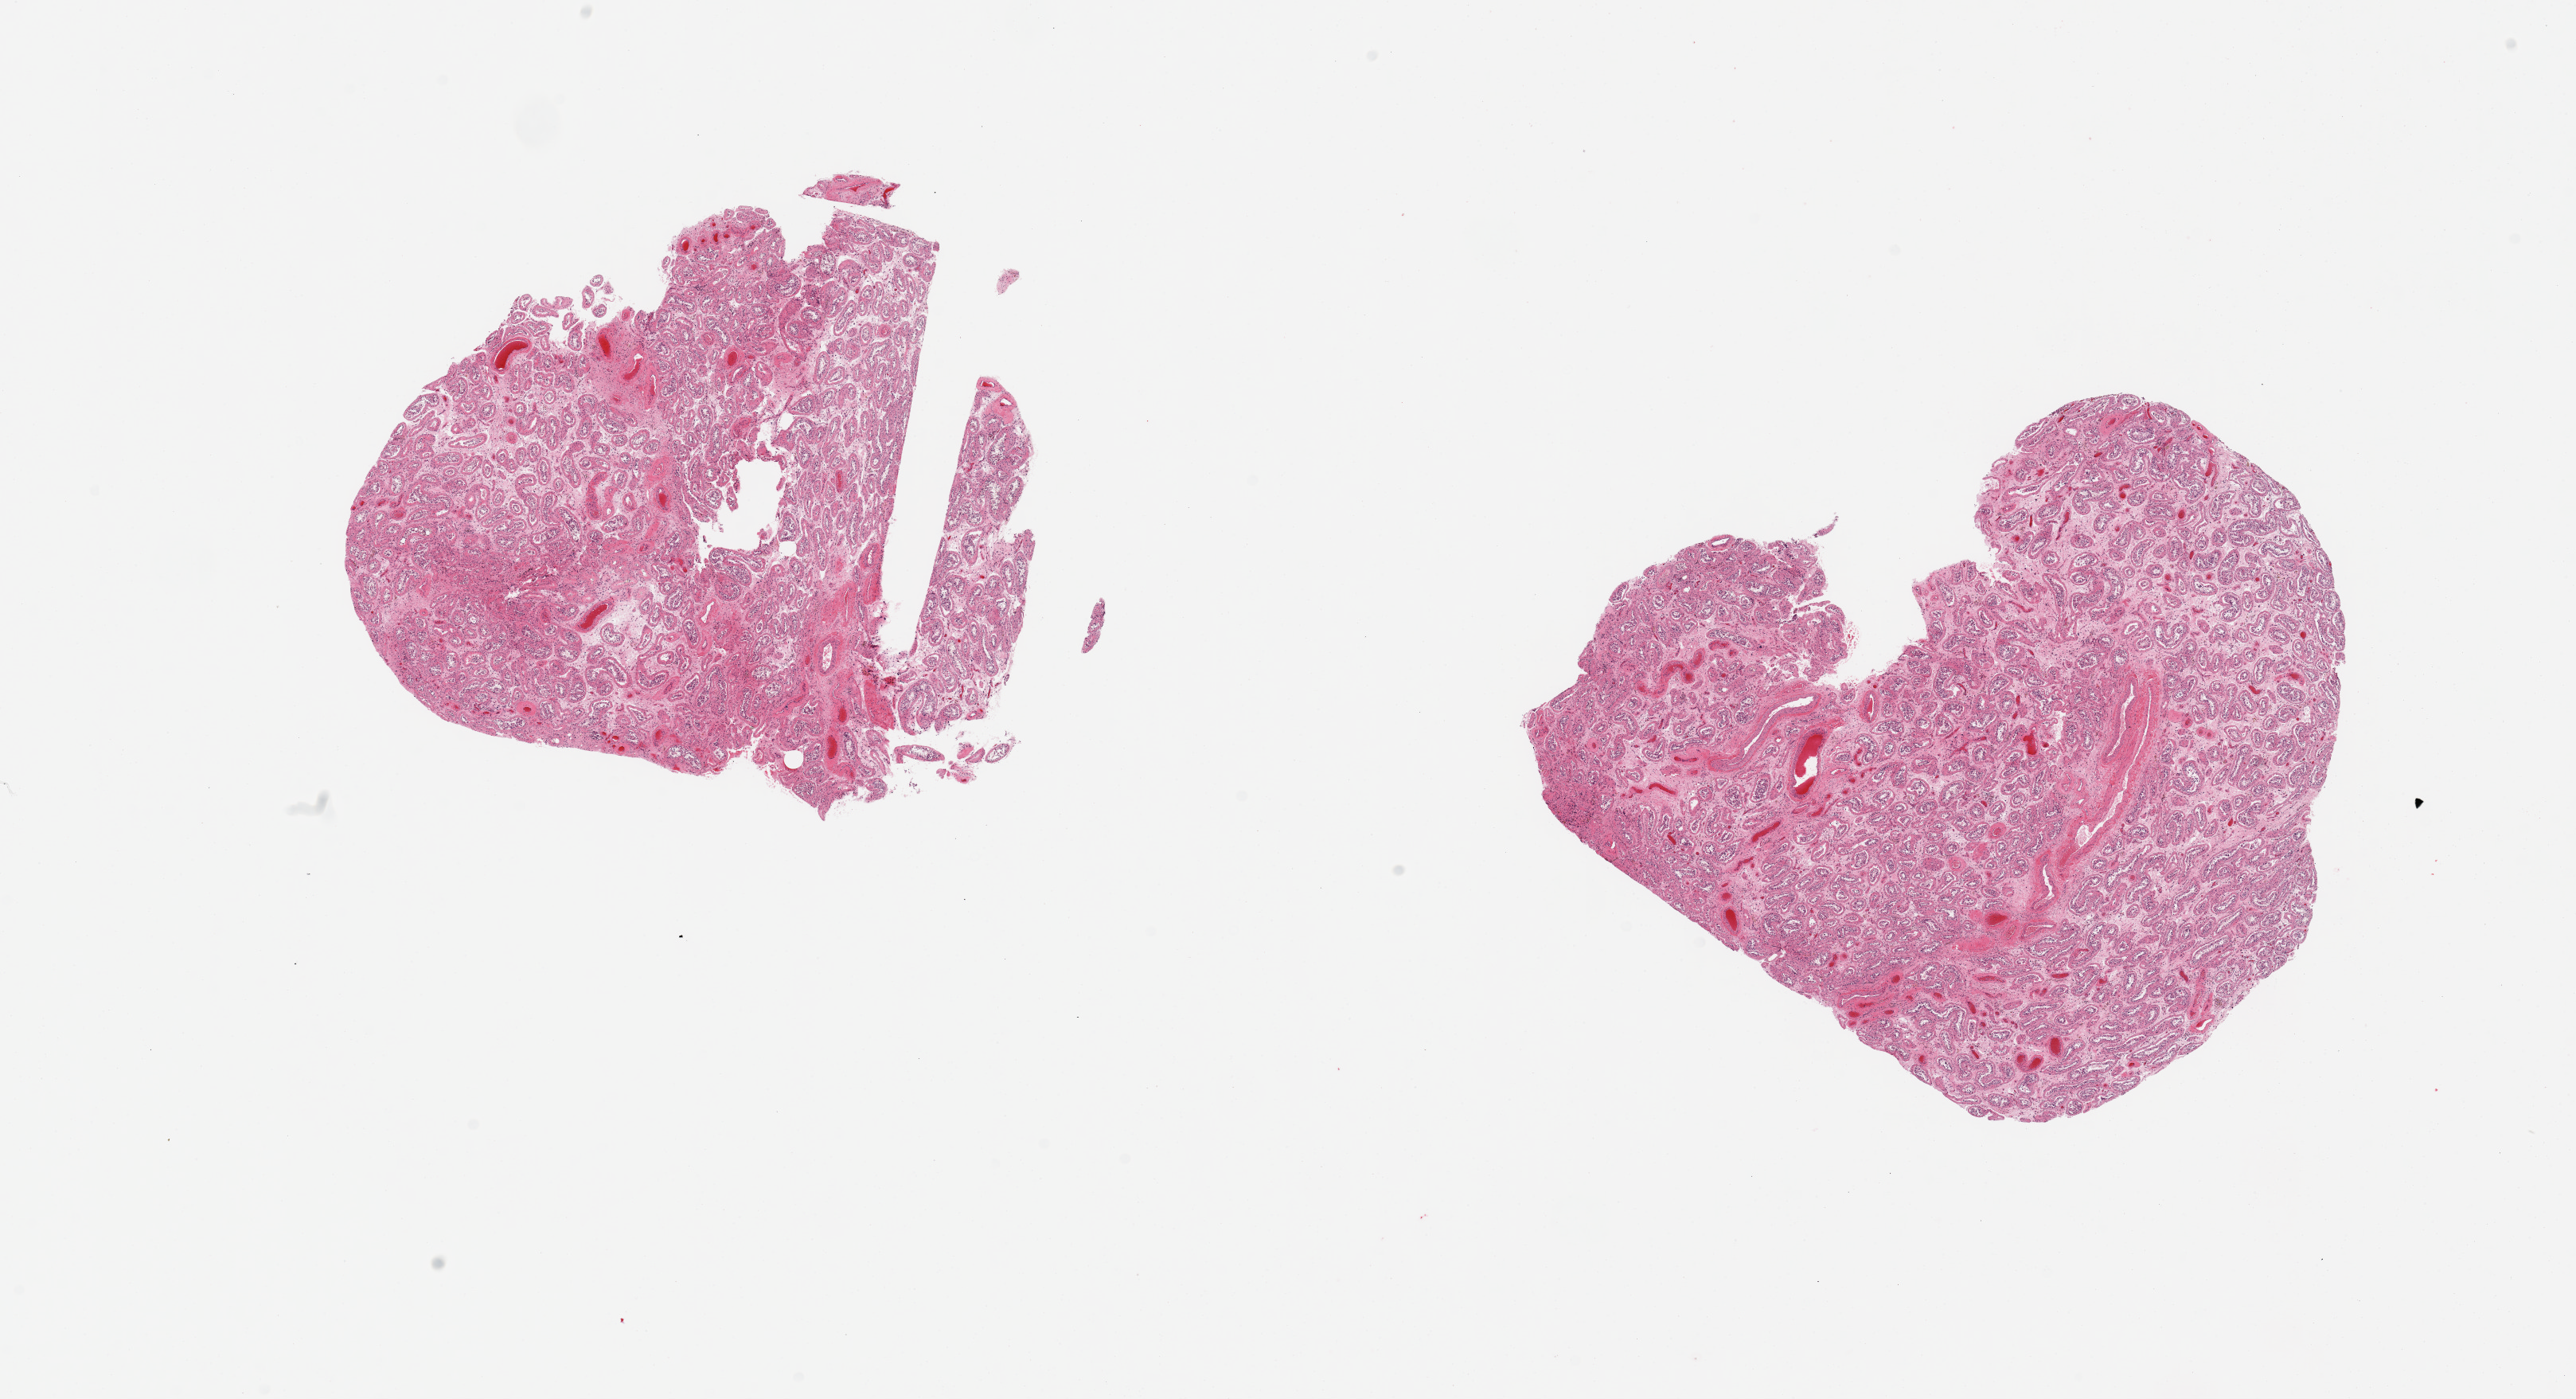
Hematoxylin and eosin (H&E) whole-slide image — whole scanned area (about 25.6 x 13.9 mm) shown as a low-resolution overview; PAXgene-fixed, paraffin-embedded tissue; target tissue: testis; donor tissue sample. Male donor.
Review note (as recorded): 2 pieces; atrophy.